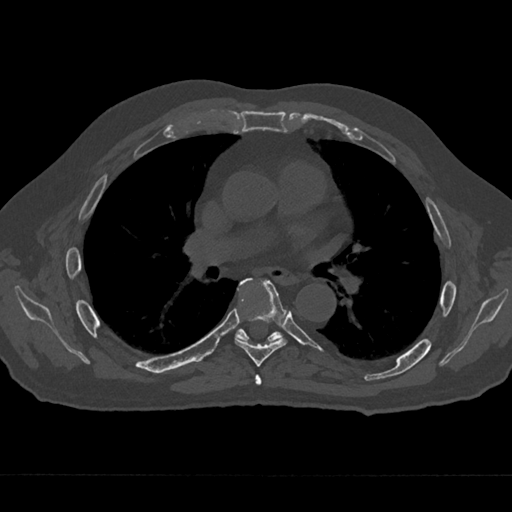
CT including the spine, one axial slice. Position 405 of 797 along the scan axis. Bone window (W 1800 / L 400 HU). 512 × 512 image matrix, field of view 377 × 377 mm. Male patient, age 75 years. From the clinical record (not read from this slice): primary cancer: renal; vertebrae with lytic lesions (as recorded): T4.
Structures marked on this image (semi-automatic segmentation, software-assisted and operator-edited):
- T5 vertebra: bounding box <255,375,262,385> (left, top, right, bottom; pixels)
- T6 vertebra: <235,278,287,367>
- T7 vertebra: <235,280,282,342>